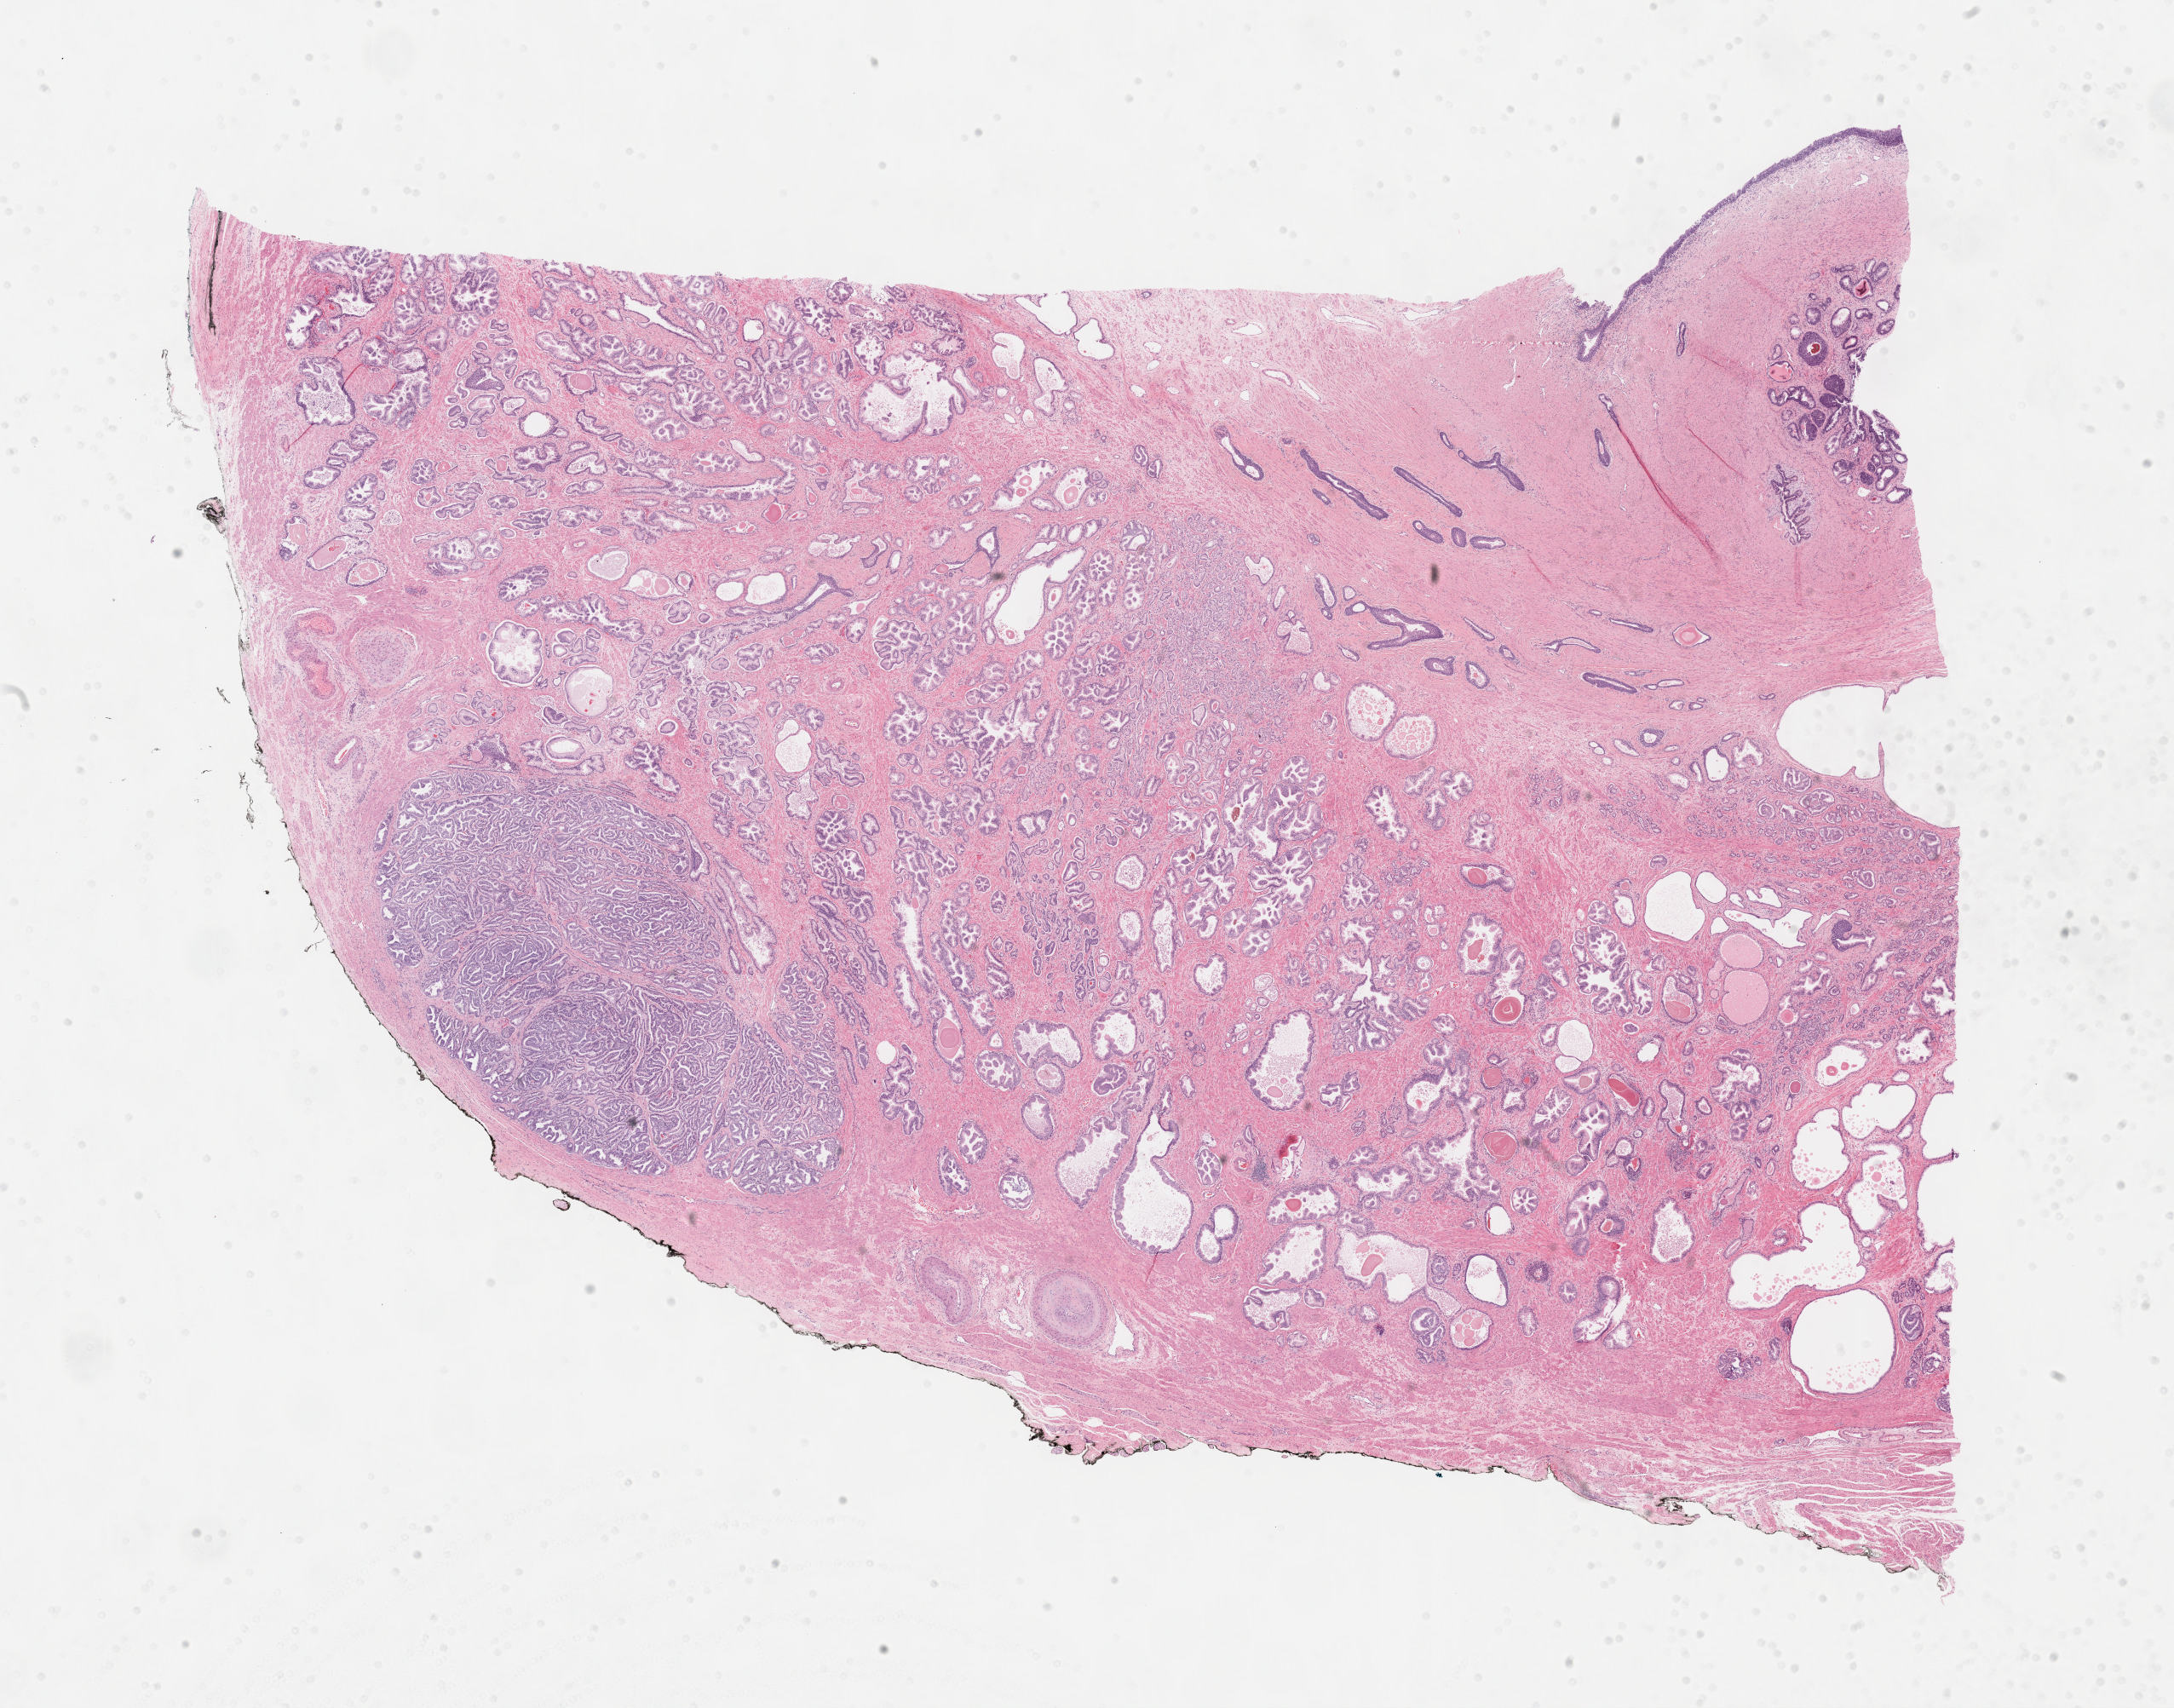
Digitized Hematoxylin and eosin (H&E) stained tissue section (whole slide), low-resolution overview of the scanned area, about 20.6 x 16.2 mm (acquisition: 40x scan); FFPE section; sample: primary tumour, prostate. Male patient; age at initial diagnosis 56 years. Gleason score: 7 (3+4).
* histologic diagnosis: Adenocarcinoma, NOS
* laterality: bilateral
* lymph nodes positive (case pathology): 1 of 15 examined